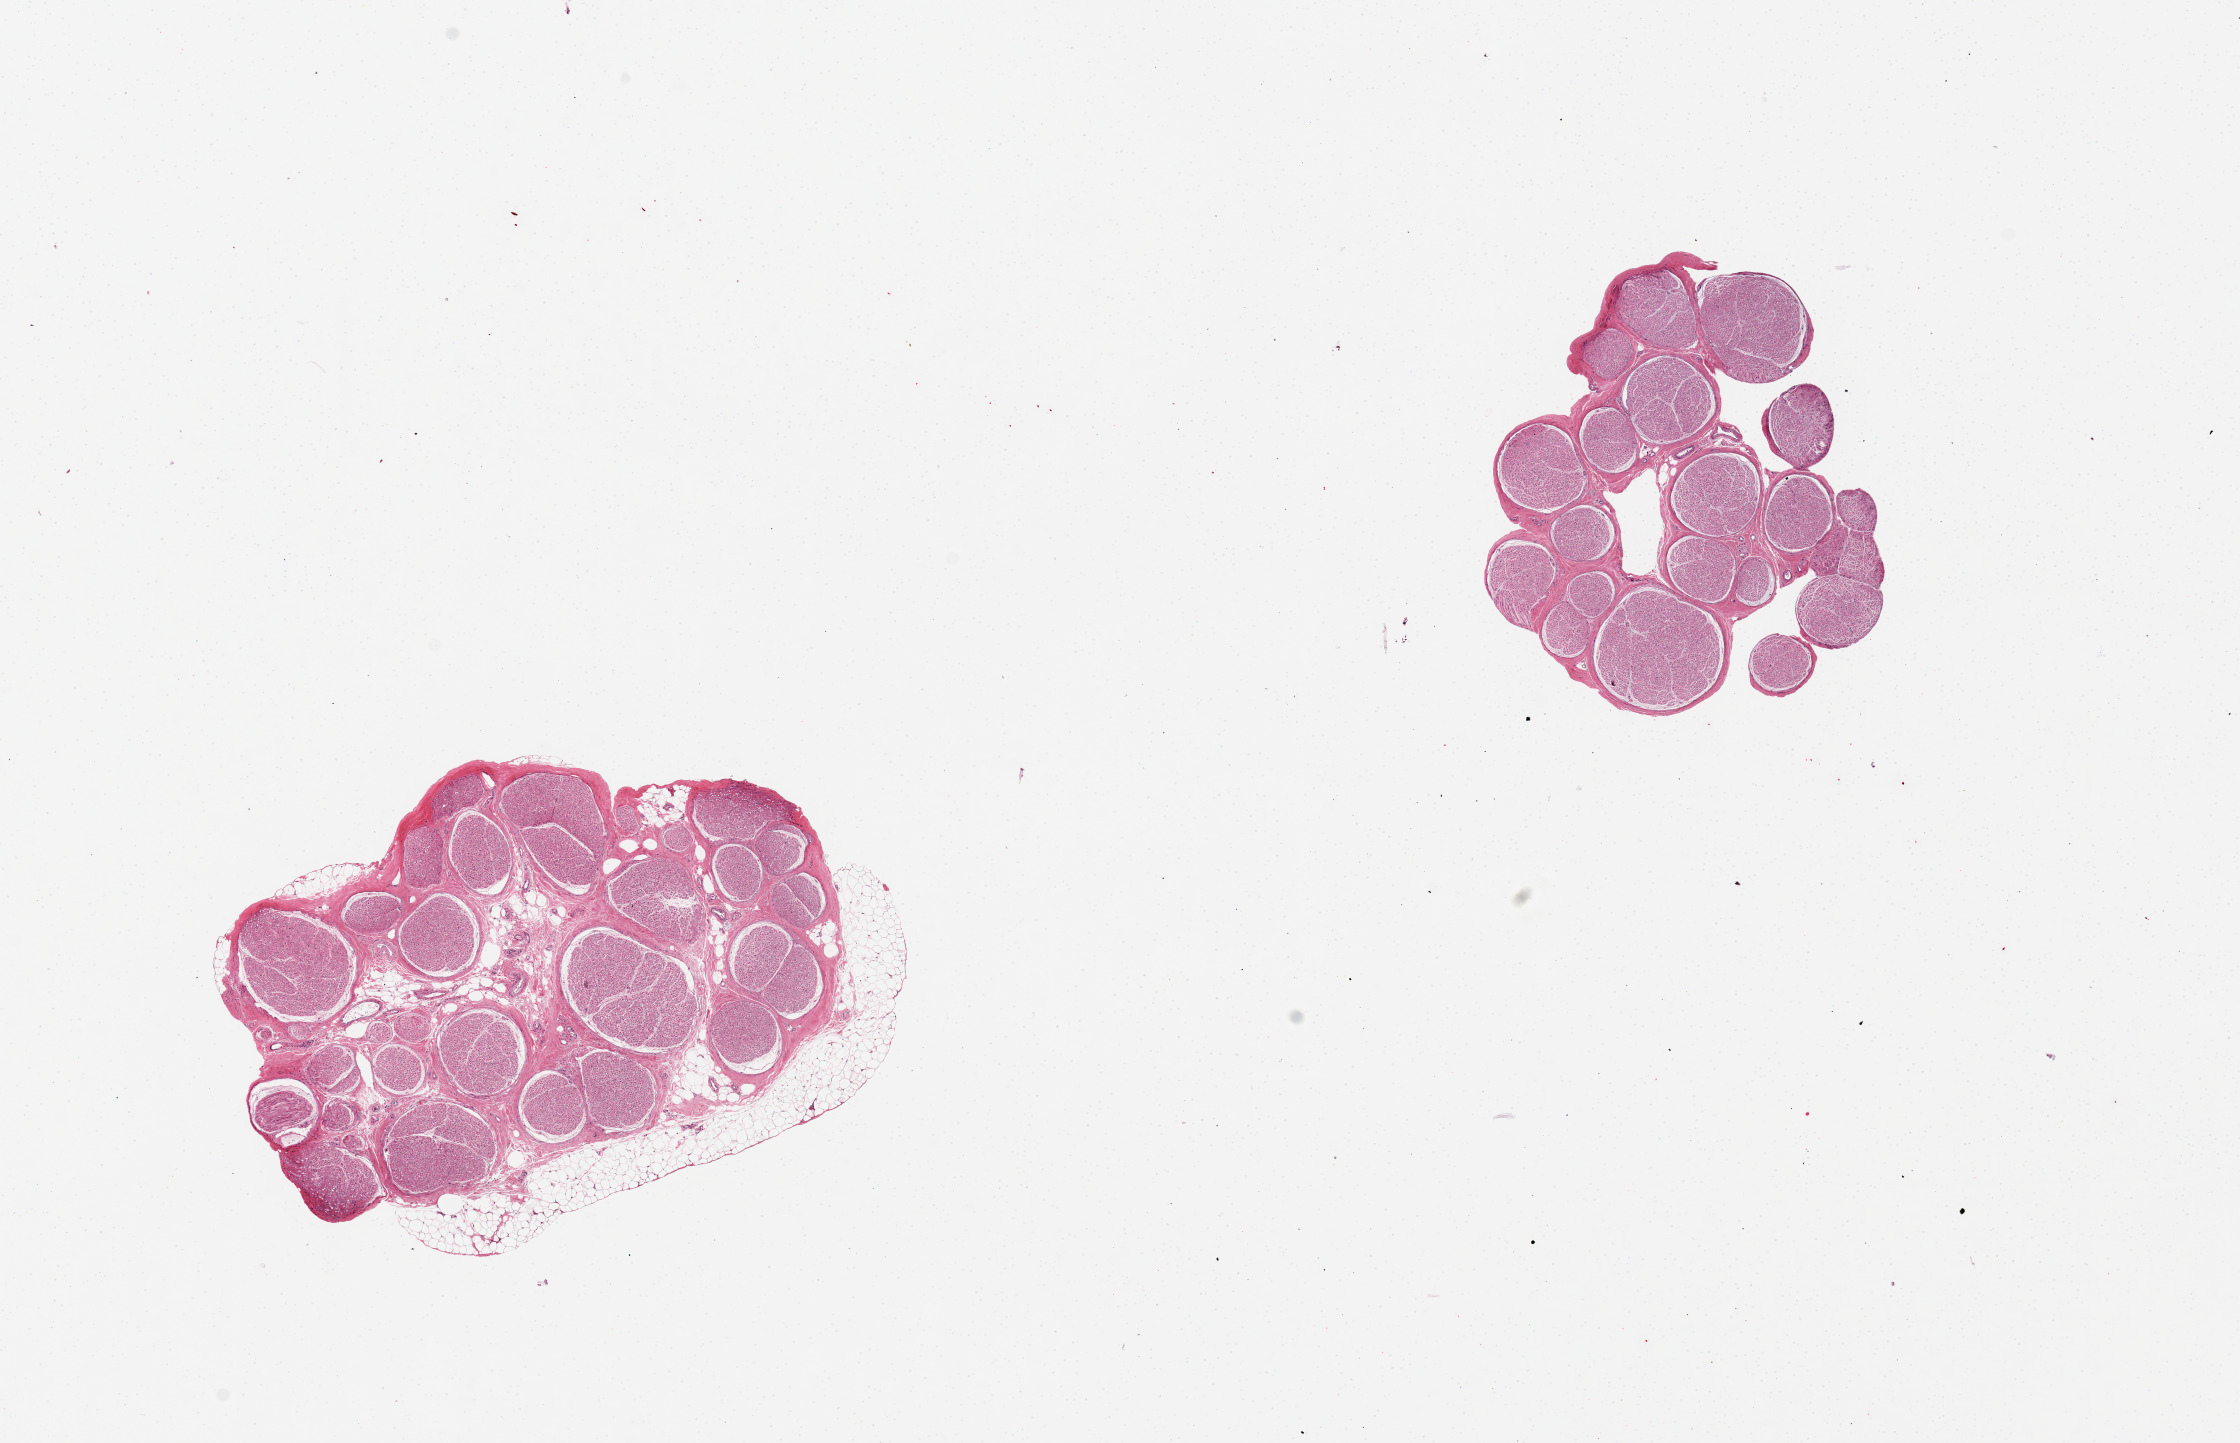
Whole-slide image, H&E stain — shown as a low-resolution overview of the whole scanned area (about 17.7 x 11.4 mm), PAXgene-fixed paraffin-embedded (PFPE) section, sampled site (target tissue): tibial nerve, donor tissue sample. Female donor.
• reviewer comment on this tissue sample: 2 pieces, one with discontinuous rim of fat, ~0.5mm